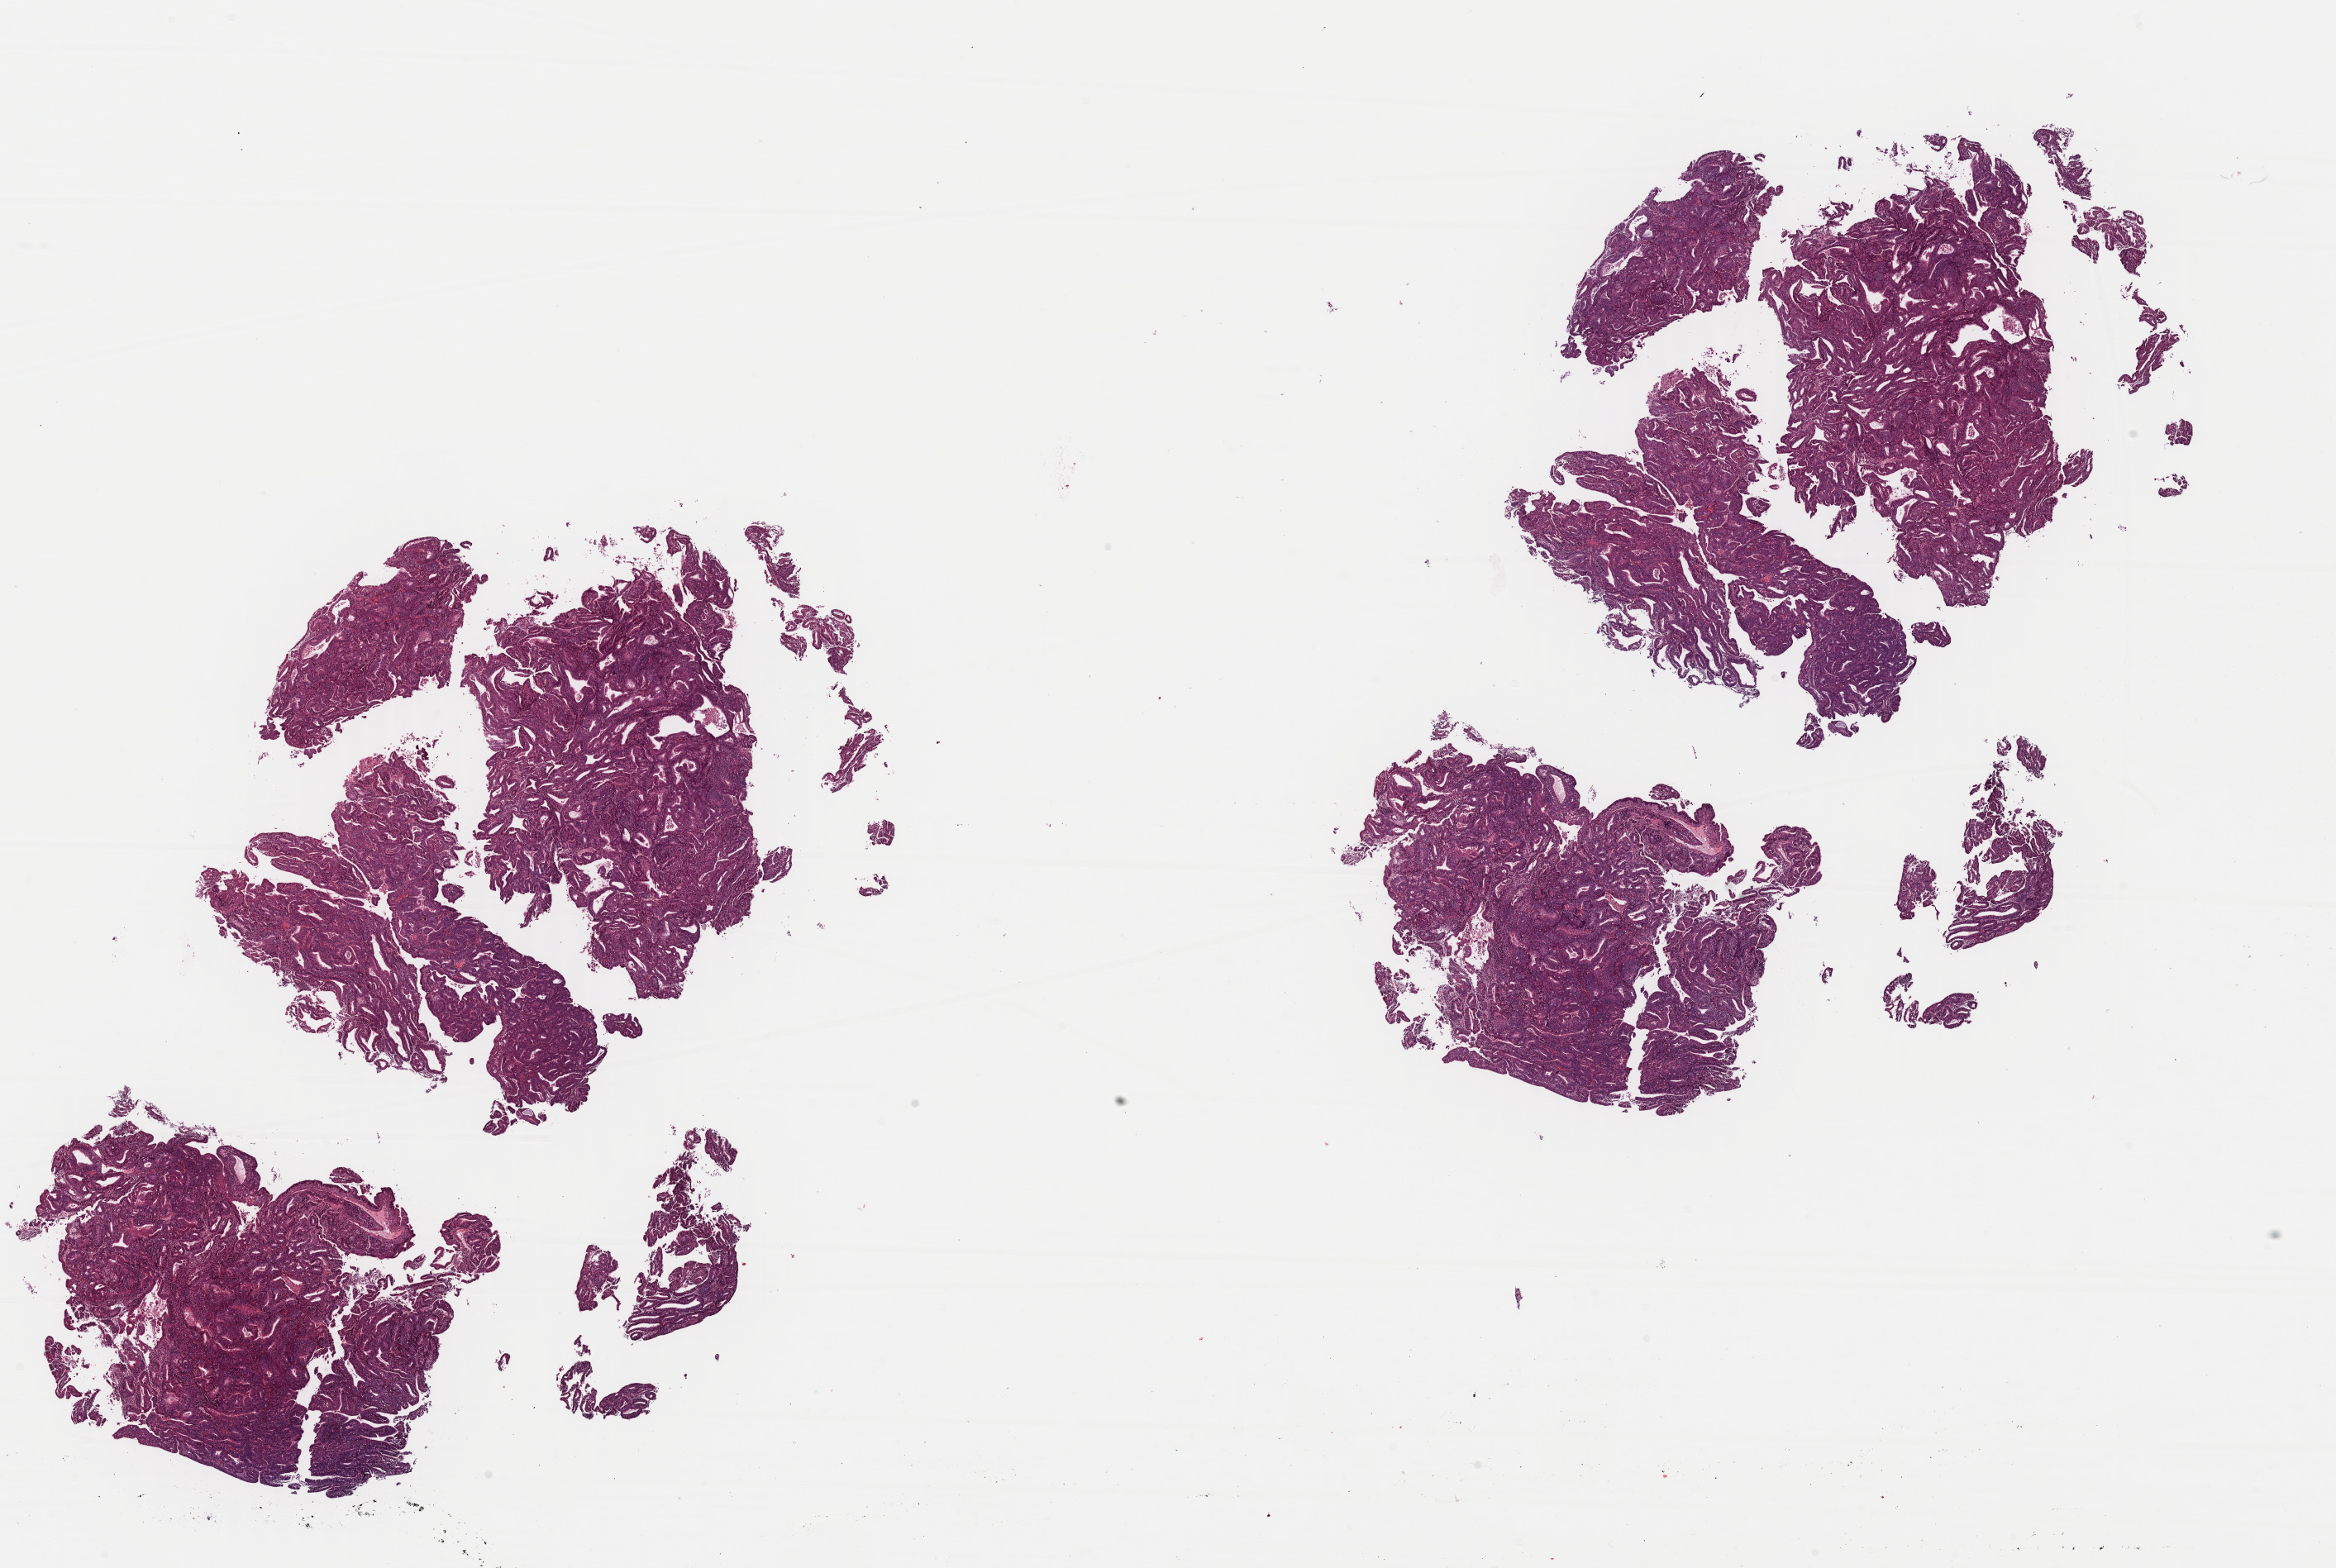
Whole-slide histology image, Hematoxylin and eosin (H&E) stained, a low-resolution overview of the entire scanned area, about 22.3 x 15.0 mm. Formalin-fixed paraffin-embedded (FFPE) diagnostic section. Uterus, primary tumour sample. Female patient; age at initial diagnosis 61 years. Histologic grade: G3 (poorly differentiated).
- FIGO stage: IIIC
- diagnosis: Serous cystadenocarcinoma, NOS (endometrium)